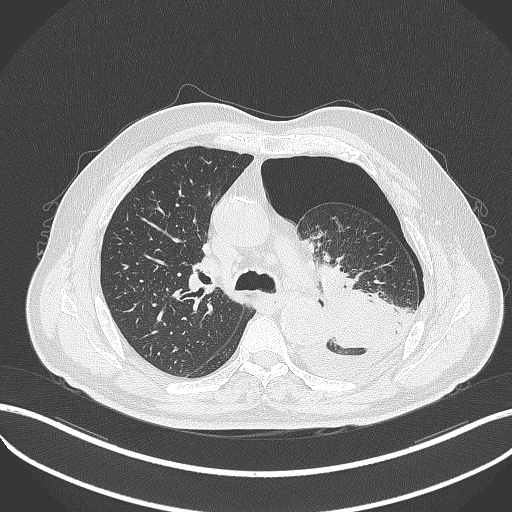
Chest CT, one axial slice. Slice 338 of 464 in the series (ordered by position). 120 kVp. Lung window (W 1500 / L -600 HU). 512 × 512 image matrix, field of view 400 × 400 mm. Male patient, age 76 years. From the clinical record (not read from this slice): clinical TNM (as recorded): T3 N0 M1b.
Structures marked on this image (bounding box drawn by a radiologist):
- lung tumour (recorded histology: adenocarcinoma): bounding box <317,273,401,347> (left, top, right, bottom; pixels)